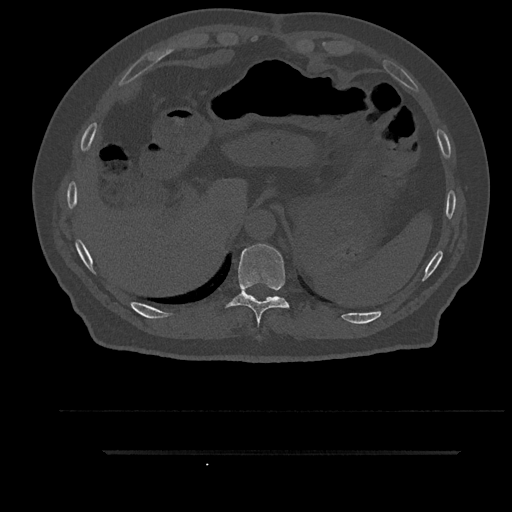
CT including the spine, one axial slice. Slice 360 of 797 in the series (ordered by position). Reconstruction kernel Br40s/3. 120 kVp. Bone window (W 1800 / L 400 HU). 0.5 mm slice thickness. 512 × 512 image matrix, field of view 432 × 432 mm. Male patient, age 63 years. Case-level facts recorded for this patient, not image findings: primary cancer: renal; vertebrae with lytic lesions (as recorded): T8.
Outlined on this slice (semi-automatic segmentation, software-assisted and operator-edited):
- T10 vertebra: bounding box <226,244,289,325> (left, top, right, bottom; pixels)